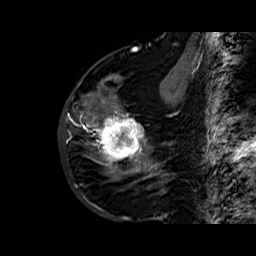
Breast MRI (dynamic contrast-enhanced), one sagittal slice. Slice 20 of 60 in the series (ordered by position). Dynamic contrast-enhanced series, time point 2 of 6 at this slice position (early post-contrast). 1.5 T. TE 6.4 ms, TR 32.8 ms. 4 mm slice thickness. 256 × 256 image matrix, field of view 200 × 200 mm. Female patient. From the clinical record (not read from this slice): setting: breast cancer imaged before/during neoadjuvant chemotherapy; receptor status: HR-positive, HER2-negative.
Structures marked on this image (semi-automatic segmentation, software-assisted and operator-edited):
- analysis volume of interest (the breast-tissue region the enhancement analysis was run in; not a lesion): bounding box (x1, y1, x2, y2) in pixels: (86, 77, 163, 177)
- tumour enhancement mask (voxels above the 100 % enhancement threshold inside the analysis volume of interest): (86, 111, 152, 176)